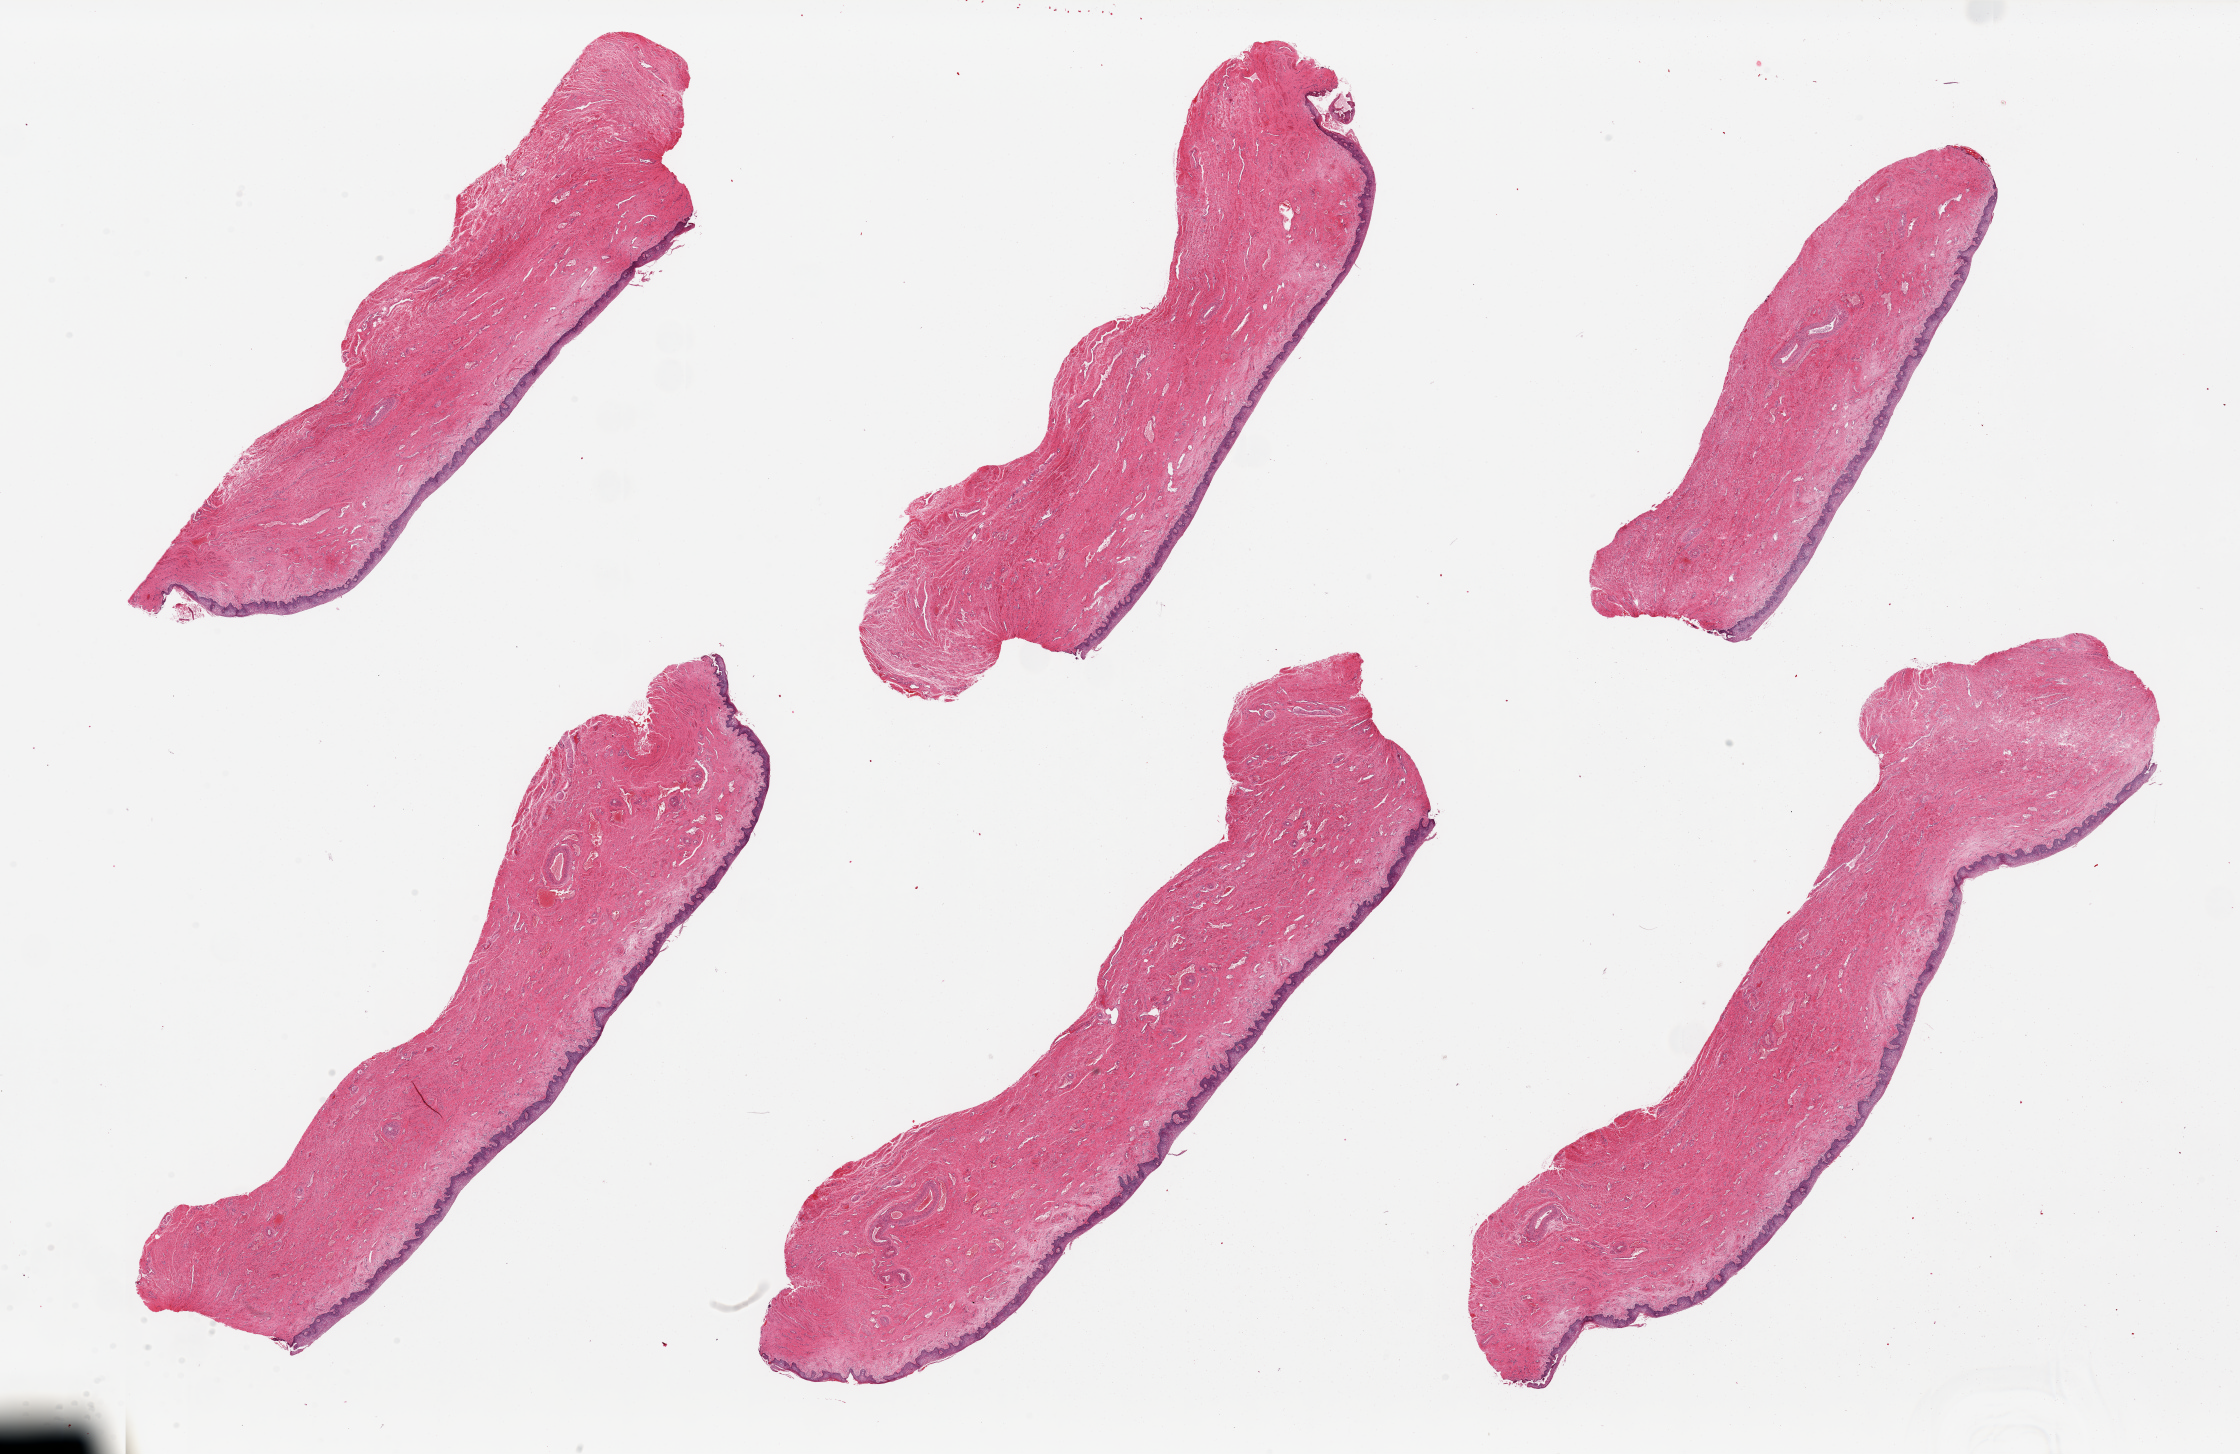
Whole-slide image, hematoxylin and eosin (H&E) stain, brightfield — whole scanned area (about 35.4 x 23.0 mm, from a 20x scan) shown as a low-resolution overview; PAXgene-fixed paraffin-embedded (PFPE) section; target tissue: vagina; donor tissue sample. Donor: female.
Pathologist's review note for this sample: 6 pieces, squamous mucosa is ~100-150microns thick.